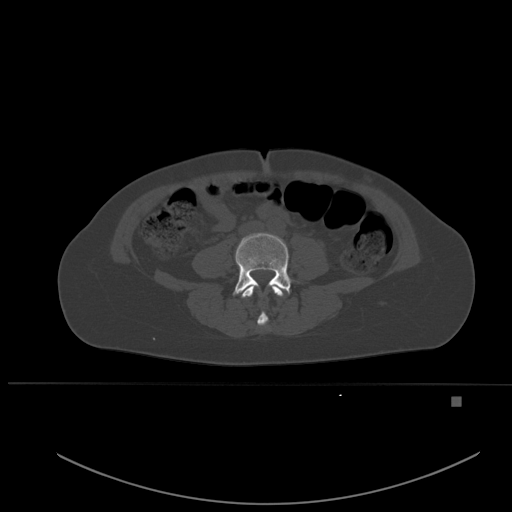
CT including the spine, one axial slice; position 178 of 651 along the scan axis; bone window (W 1800 / L 400 HU); 512 × 512 image matrix. Patient: female, 49 years. From the clinical record (not read from this slice): primary cancer: breast; vertebrae with lytic lesions (as recorded): L3, T12, L4.
Annotated regions visible in this slice (semi-automatically segmented with operator editing):
- L3 vertebra: bounding box <241,285,284,326> (left, top, right, bottom; pixels)
- L4 vertebra: <233,233,291,295>